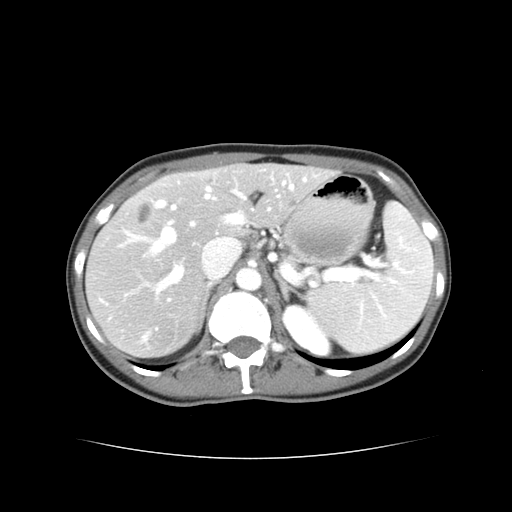
Contrast-enhanced abdominal CT, one axial slice. Position 25 of 38 along the scan axis. 120 kVp. Intravenous contrast given. Soft-tissue window (W 400 / L 40 HU). 5 mm slice thickness. 512 × 512 image matrix, field of view 340 × 340 mm. Female patient, age 54 years. From the clinical record (not read from this slice): diagnosis: colorectal cancer liver metastases, imaged before liver resection; multiple liver metastases: yes; largest metastasis: 1.1 cm; disease in both lobes: yes.
Annotated regions visible in this slice (outlined manually by an expert reader):
- hepatic veins: bounding box (x1, y1, x2, y2) in pixels: (127, 185, 294, 252)
- liver: (88, 165, 329, 358)
- planned liver remnant (the part of the liver to remain after resection): (213, 165, 329, 232)
- portal vein (with intrahepatic branches): (152, 179, 307, 292)
- liver metastasis: (139, 204, 151, 222)